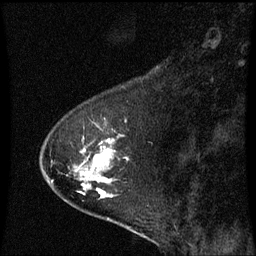
Breast MRI (dynamic contrast-enhanced), one sagittal slice; slice 17 of 60 in the series (ordered by position); dynamic contrast-enhanced series, image 2 of 3 at this slice position (ordered by acquisition); 1.5 T; TE 4.2 ms, TR 8.9 ms; 256 × 256 image matrix, field of view 200 × 200 mm. Female patient, age 53 years. From the clinical record (not read from this slice): setting: breast cancer imaged before/during neoadjuvant chemotherapy; receptor status: HR-positive, HER2-negative.
Structures marked on this image (semi-automatically segmented with operator editing):
- analysis volume of interest (the breast-tissue region the enhancement analysis was run in; not a lesion): bounding box [x1, y1, x2, y2] px = [40, 120, 129, 221]
- tumour enhancement mask (voxels above the 70 % enhancement threshold inside the analysis volume of interest): [84, 150, 111, 197]